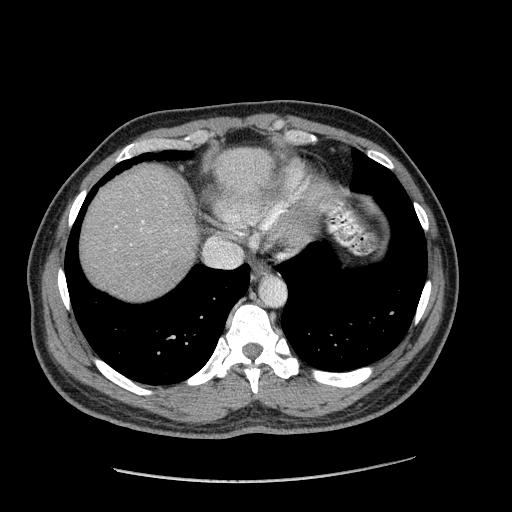
Contrast-enhanced abdominal CT (liver protocol), one axial slice. Position 159 of 182 along the scan axis. Reconstruction kernel STANDARD. 120 kVp. Soft-tissue window (W 400 / L 40 HU). 2.5 mm slice thickness. 512 × 512 image matrix. Case-level facts recorded for this patient, not image findings: diagnosis: hepatocellular carcinoma (patient treated with transarterial chemoembolisation; whether this scan precedes or follows treatment is not stated here); TNM stage (as recorded): Stage-I; Child-Pugh class: A; tumour differentiation: well differentiated; tumour size: 3.1 cm.
Structures marked on this image (semi-automatic segmentation, software-assisted and operator-edited):
- abdominal aorta: bounding box <260,277,286,306> (left, top, right, bottom; pixels)
- liver parenchyma outside the tumour (the mass and vessels are separate outlines, so this box may not span the whole liver): <80,148,272,300>